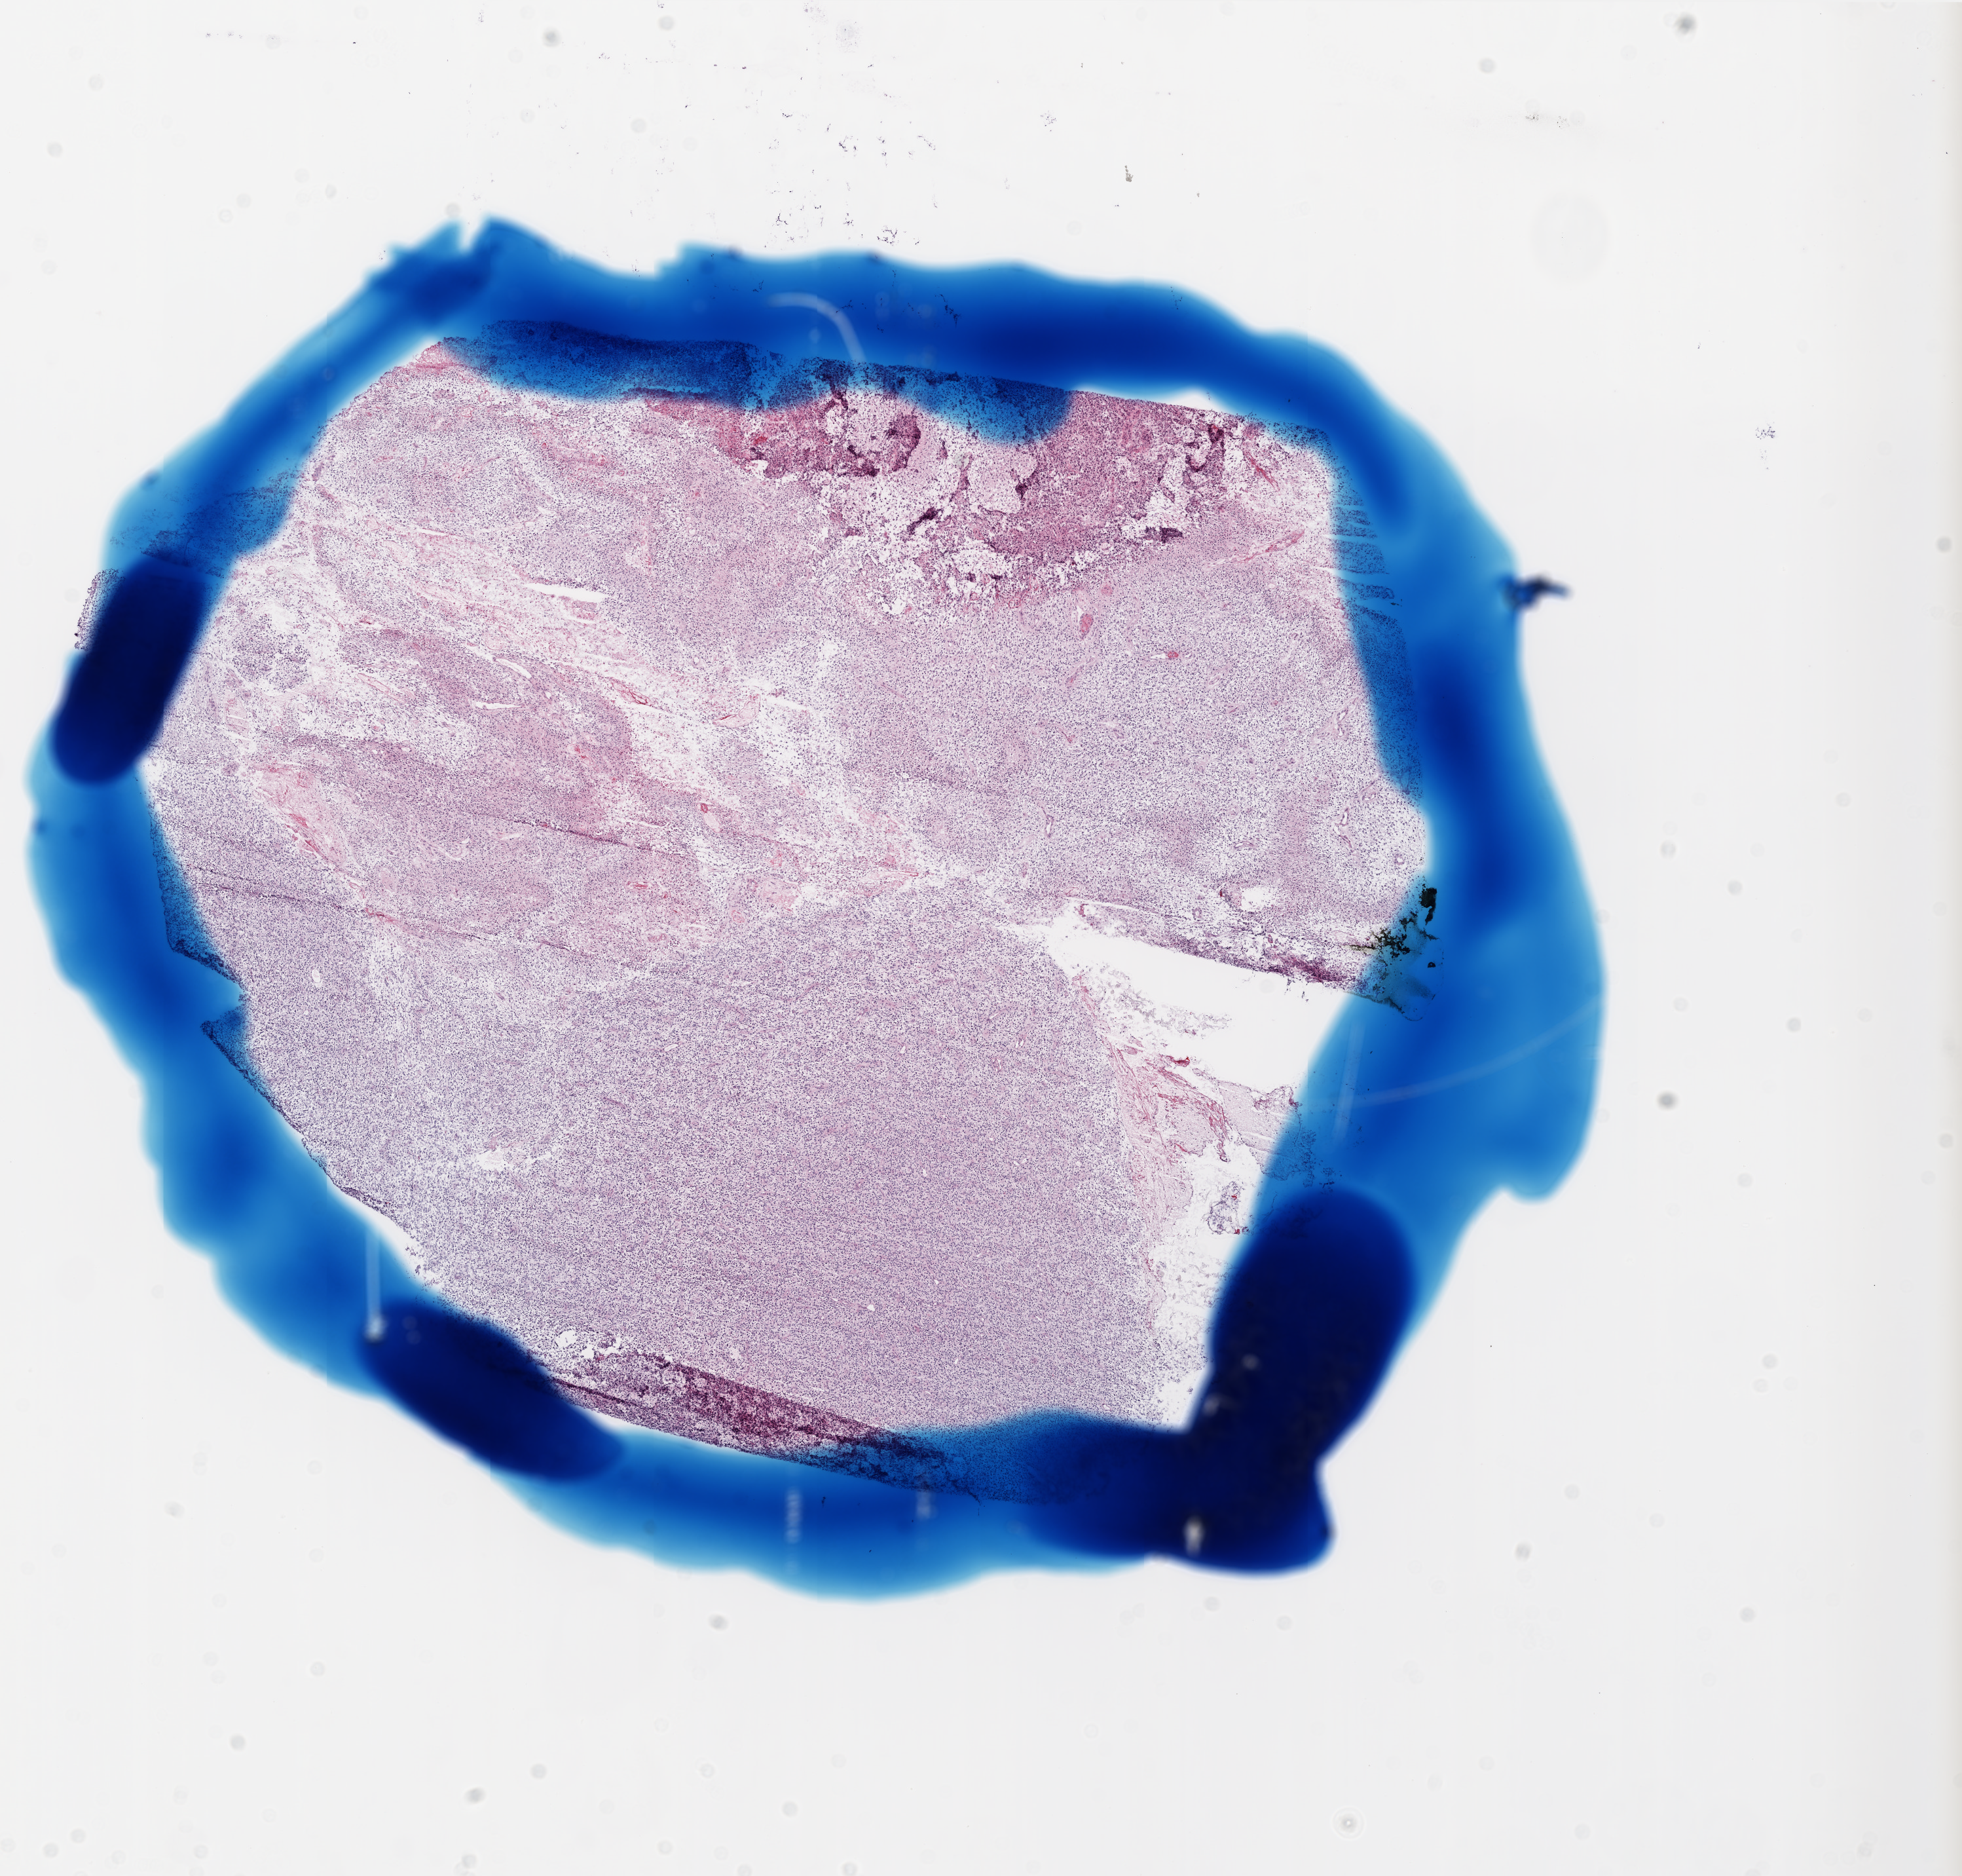
Hematoxylin and eosin (H&E) stained whole-slide image — low-resolution overview of the scanned area, about 12.0 x 11.5 mm; frozen section; sample: primary tumour, brain. Female, age 63 years at initial diagnosis. Composition of this section per pathologist review: tumour cells 95%, tumour nuclei 100%, normal cells 0%, stromal cells 0%, necrosis 5%.
Histologic diagnosis: Glioblastoma.